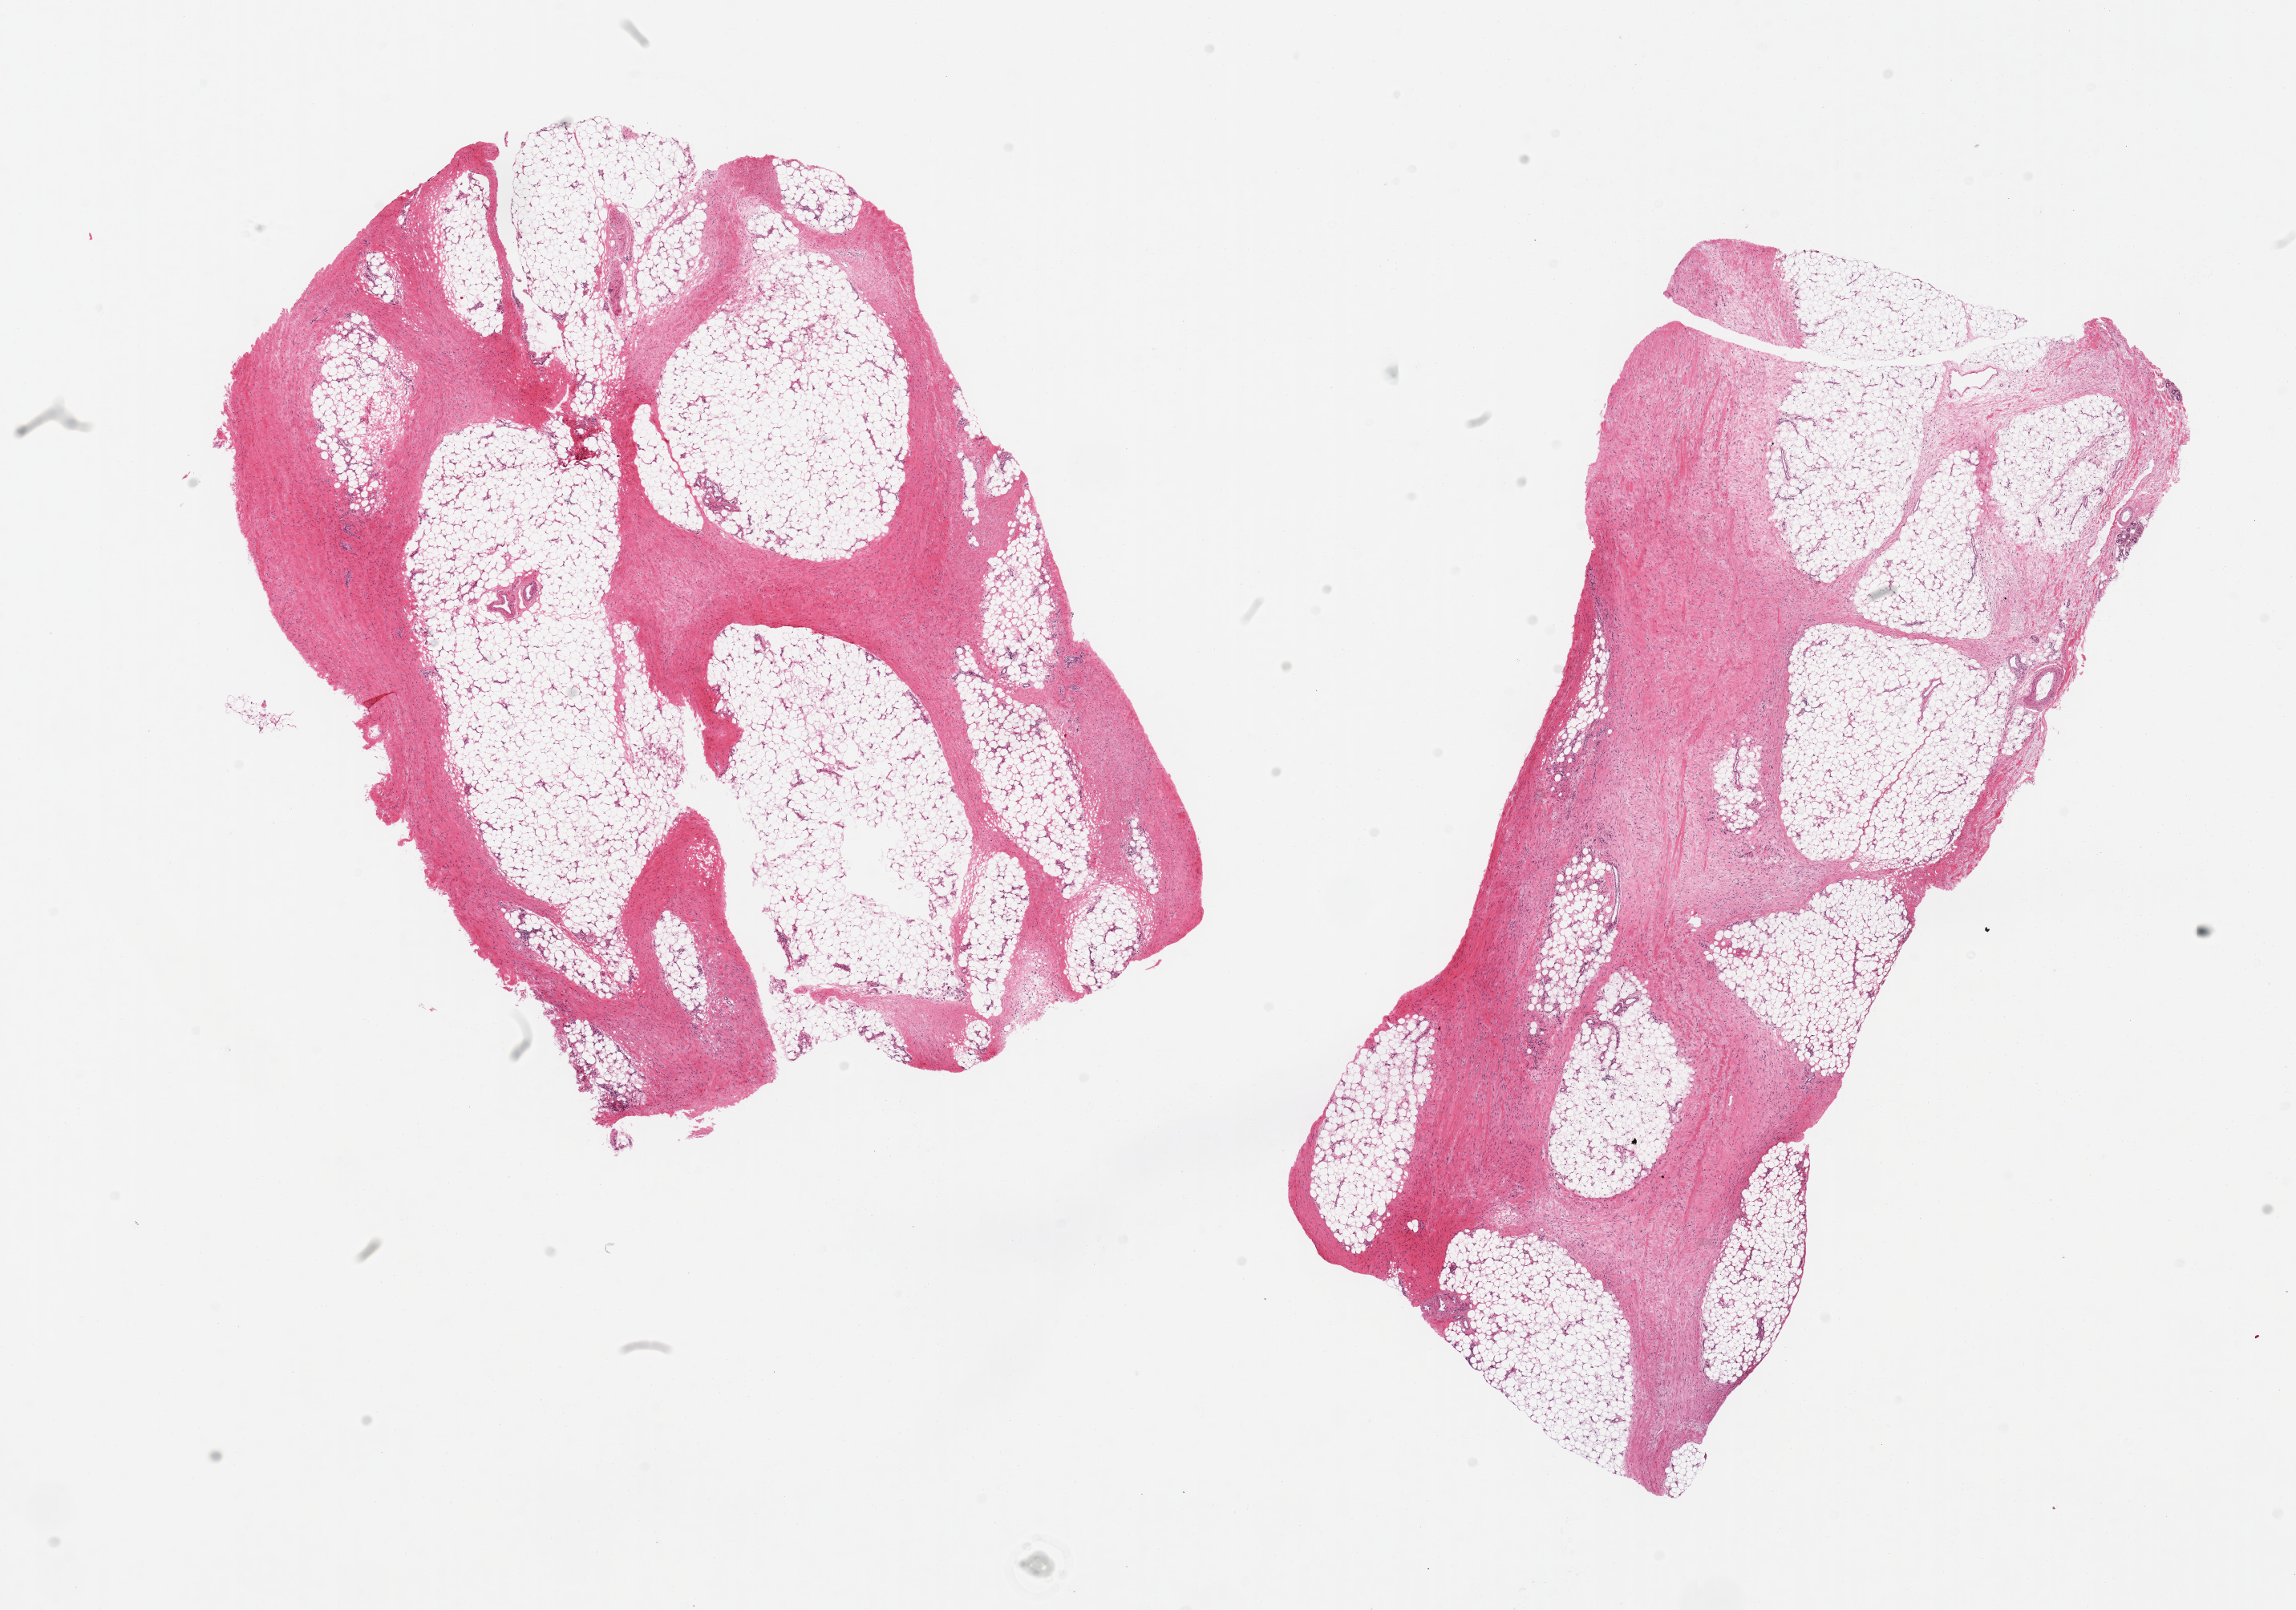
Whole-slide image, H&E stain, whole scanned area (about 22.6 x 15.9 mm, from a 20x scan) shown as a low-resolution overview; PAXgene-fixed, paraffin-embedded tissue; target tissue: adipose tissue; tissue donor sample.
Review note (as recorded): 2 pieces; septal fibrosis compromising significantly fat lobules.